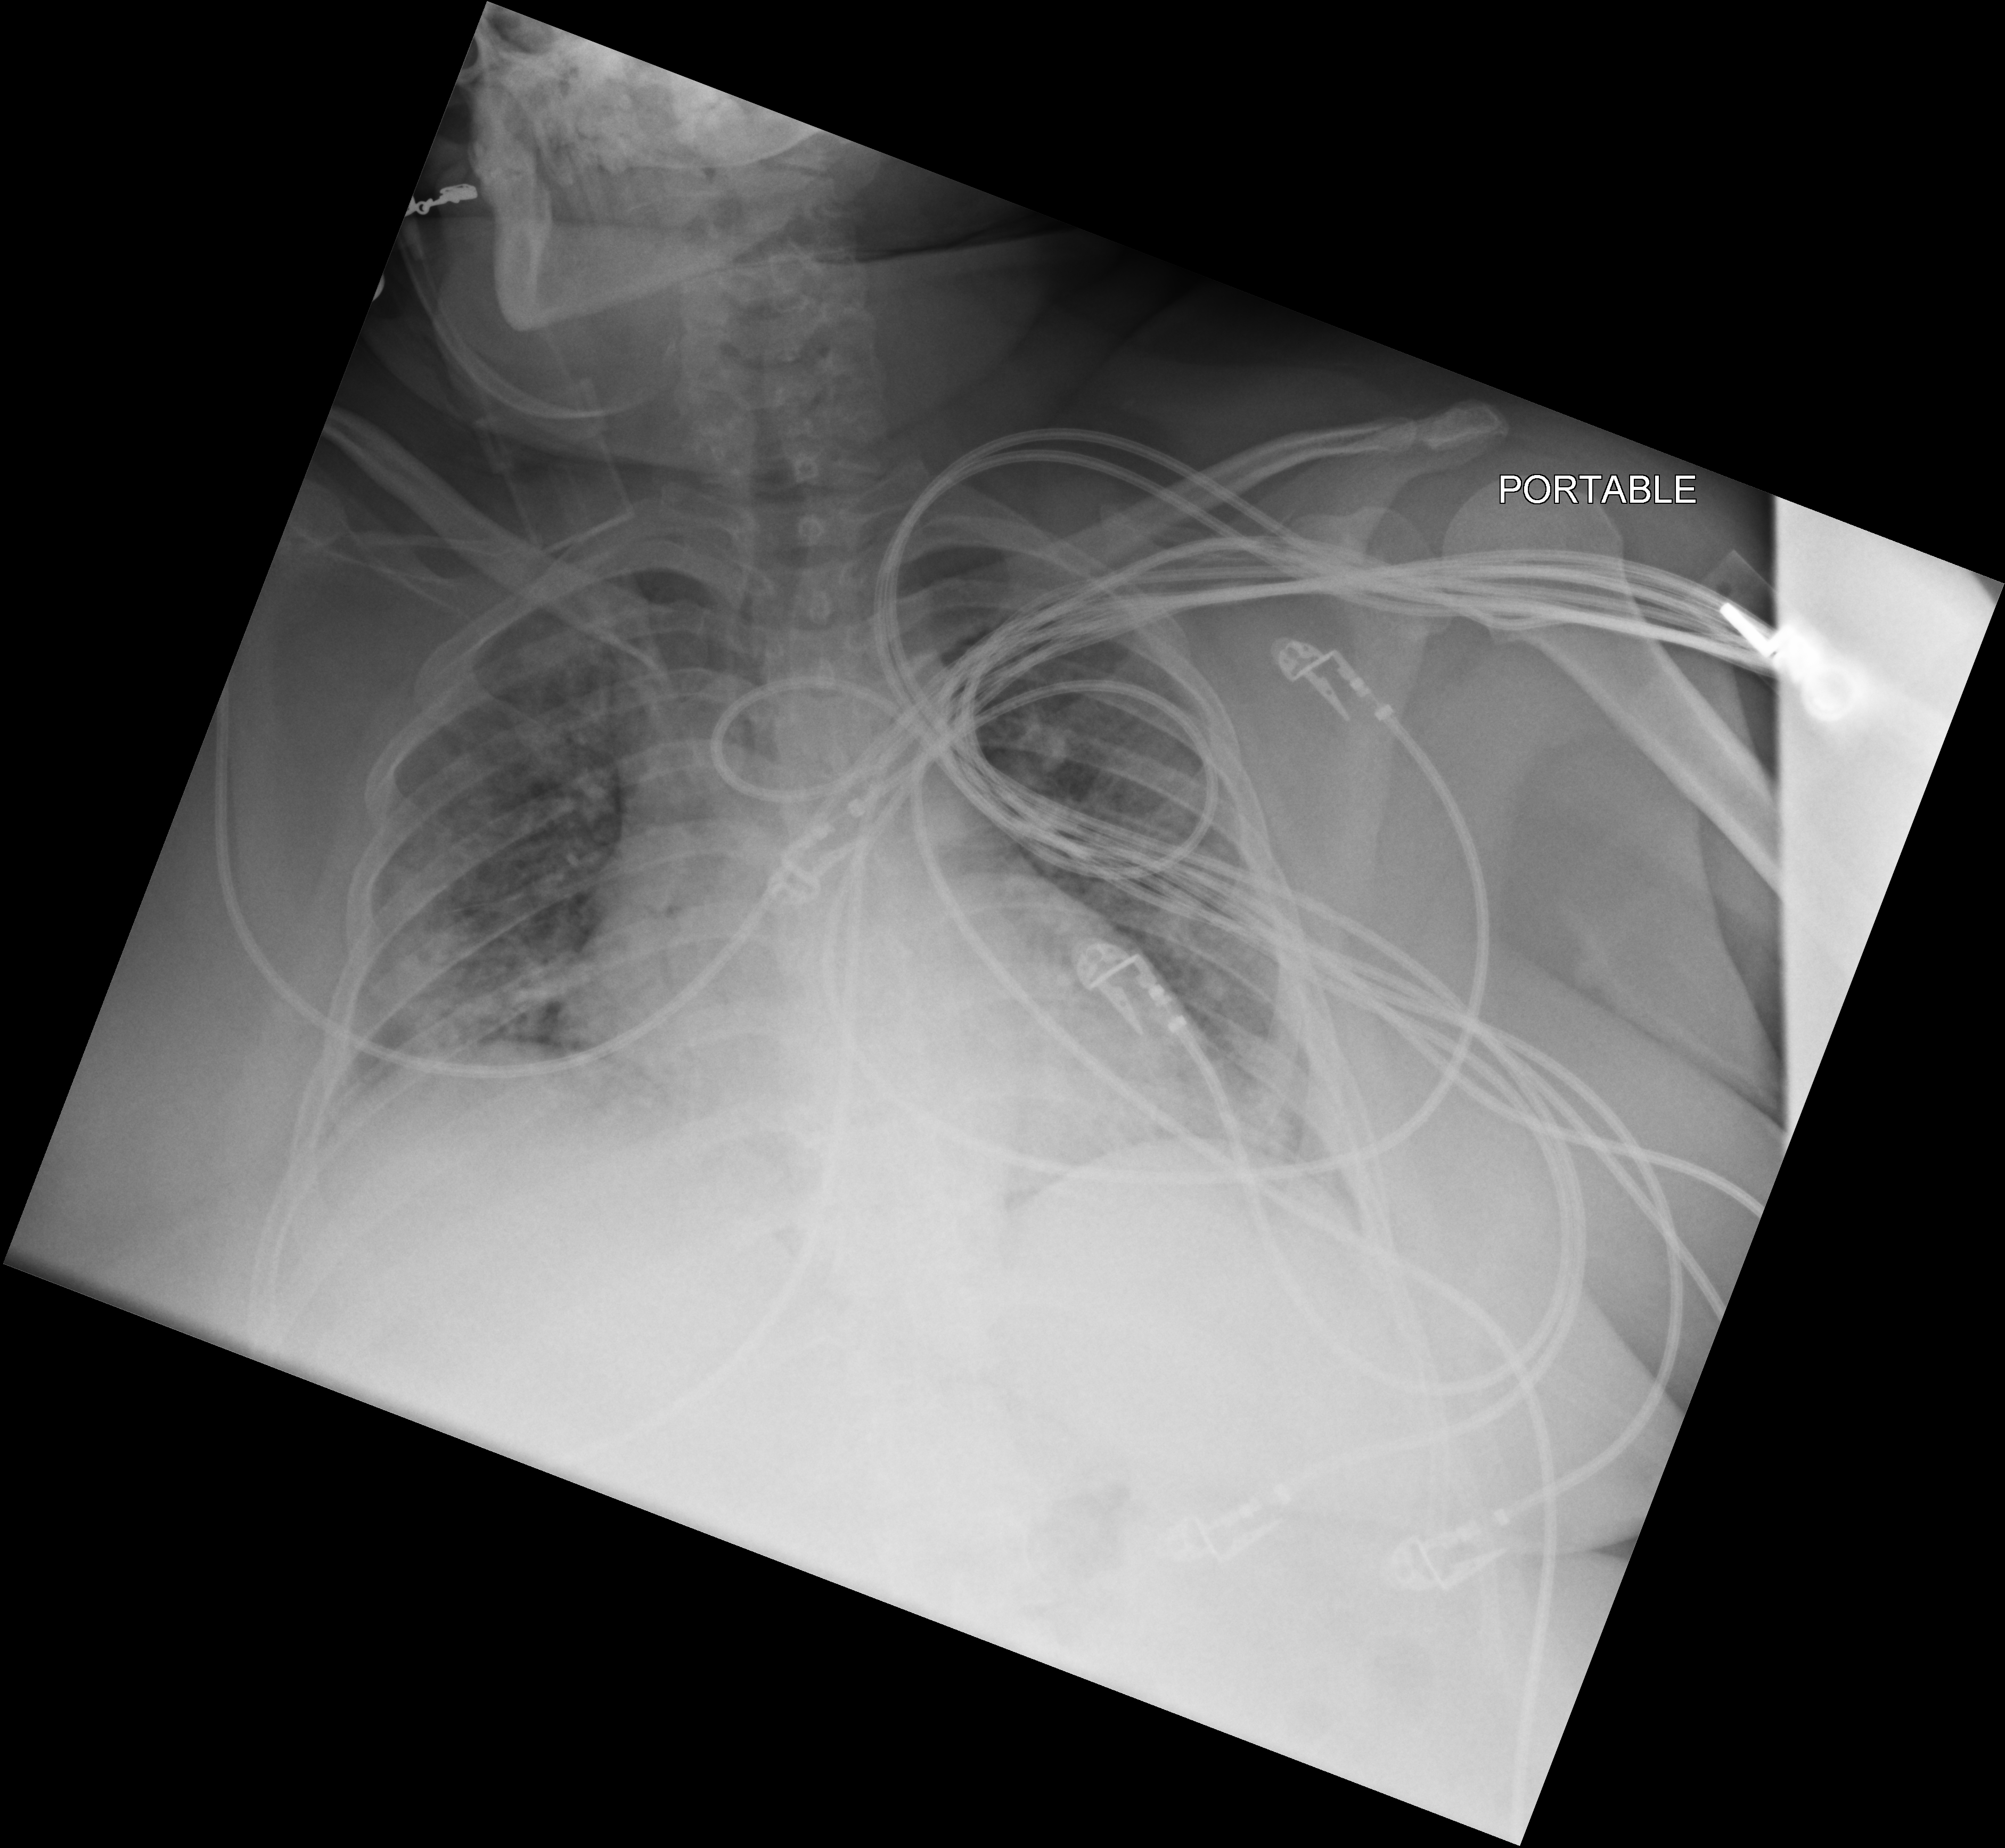
Bedside chest radiograph (computed radiography). Patient hospitalised with COVID-19; female, aged 18–59 years.
Hospital-stay facts (about this admission, not read from this image; timing relative to this image not recorded):
- mechanically ventilated during this hospital stay: yes